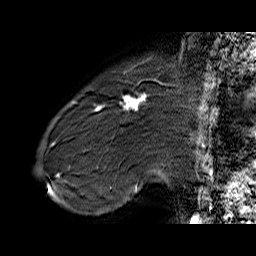
Breast MRI (dynamic contrast-enhanced), one sagittal slice. Position 14 of 60 along the scan axis. Dynamic contrast-enhanced series, time point 2 of 6 at this slice position (early post-contrast). 1.5 T. TE 6.4 ms, TR 32.9 ms. 4 mm slice thickness. 256 × 256 image matrix, field of view 200 × 200 mm. Female patient. From the clinical record (not read from this slice): setting: breast cancer imaged before/during neoadjuvant chemotherapy; receptor status: HER2-positive.
Structures marked on this image (semi-automatically segmented with operator editing):
- analysis volume of interest (the breast-tissue region the enhancement analysis was run in; not a lesion): bounding box [x1, y1, x2, y2] px = [71, 80, 155, 146]
- tumour enhancement mask (voxels above the 100 % enhancement threshold inside the analysis volume of interest): [95, 94, 147, 110]